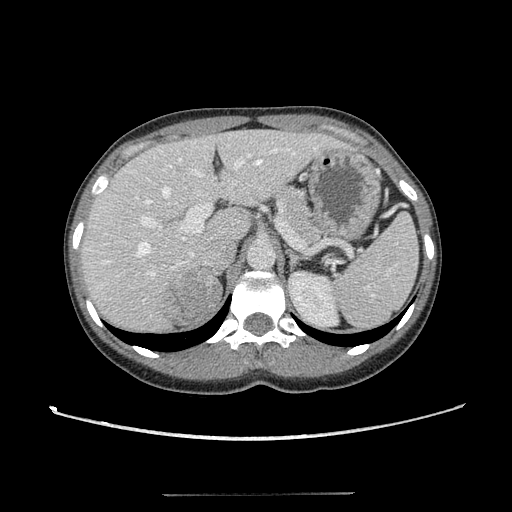
Contrast-enhanced abdominal CT, one axial slice; slice 79 of 117 in the series (ordered by position); intravenous contrast given; soft-tissue window (W 400 / L 40 HU); 512 × 512 image matrix, field of view 365 × 365 mm. Female patient, age 35 years. Case-level facts recorded for this patient, not image findings: diagnosis: adrenocortical carcinoma; tumour side: right adrenal; tumour size at pathology: 3 cm; Ki-67 index: 21 %; stage (as recorded): 3.
Structures marked on this image (semi-automatically segmented with operator editing):
- mass: box from (x=162, y=276) to (x=222, y=323) px